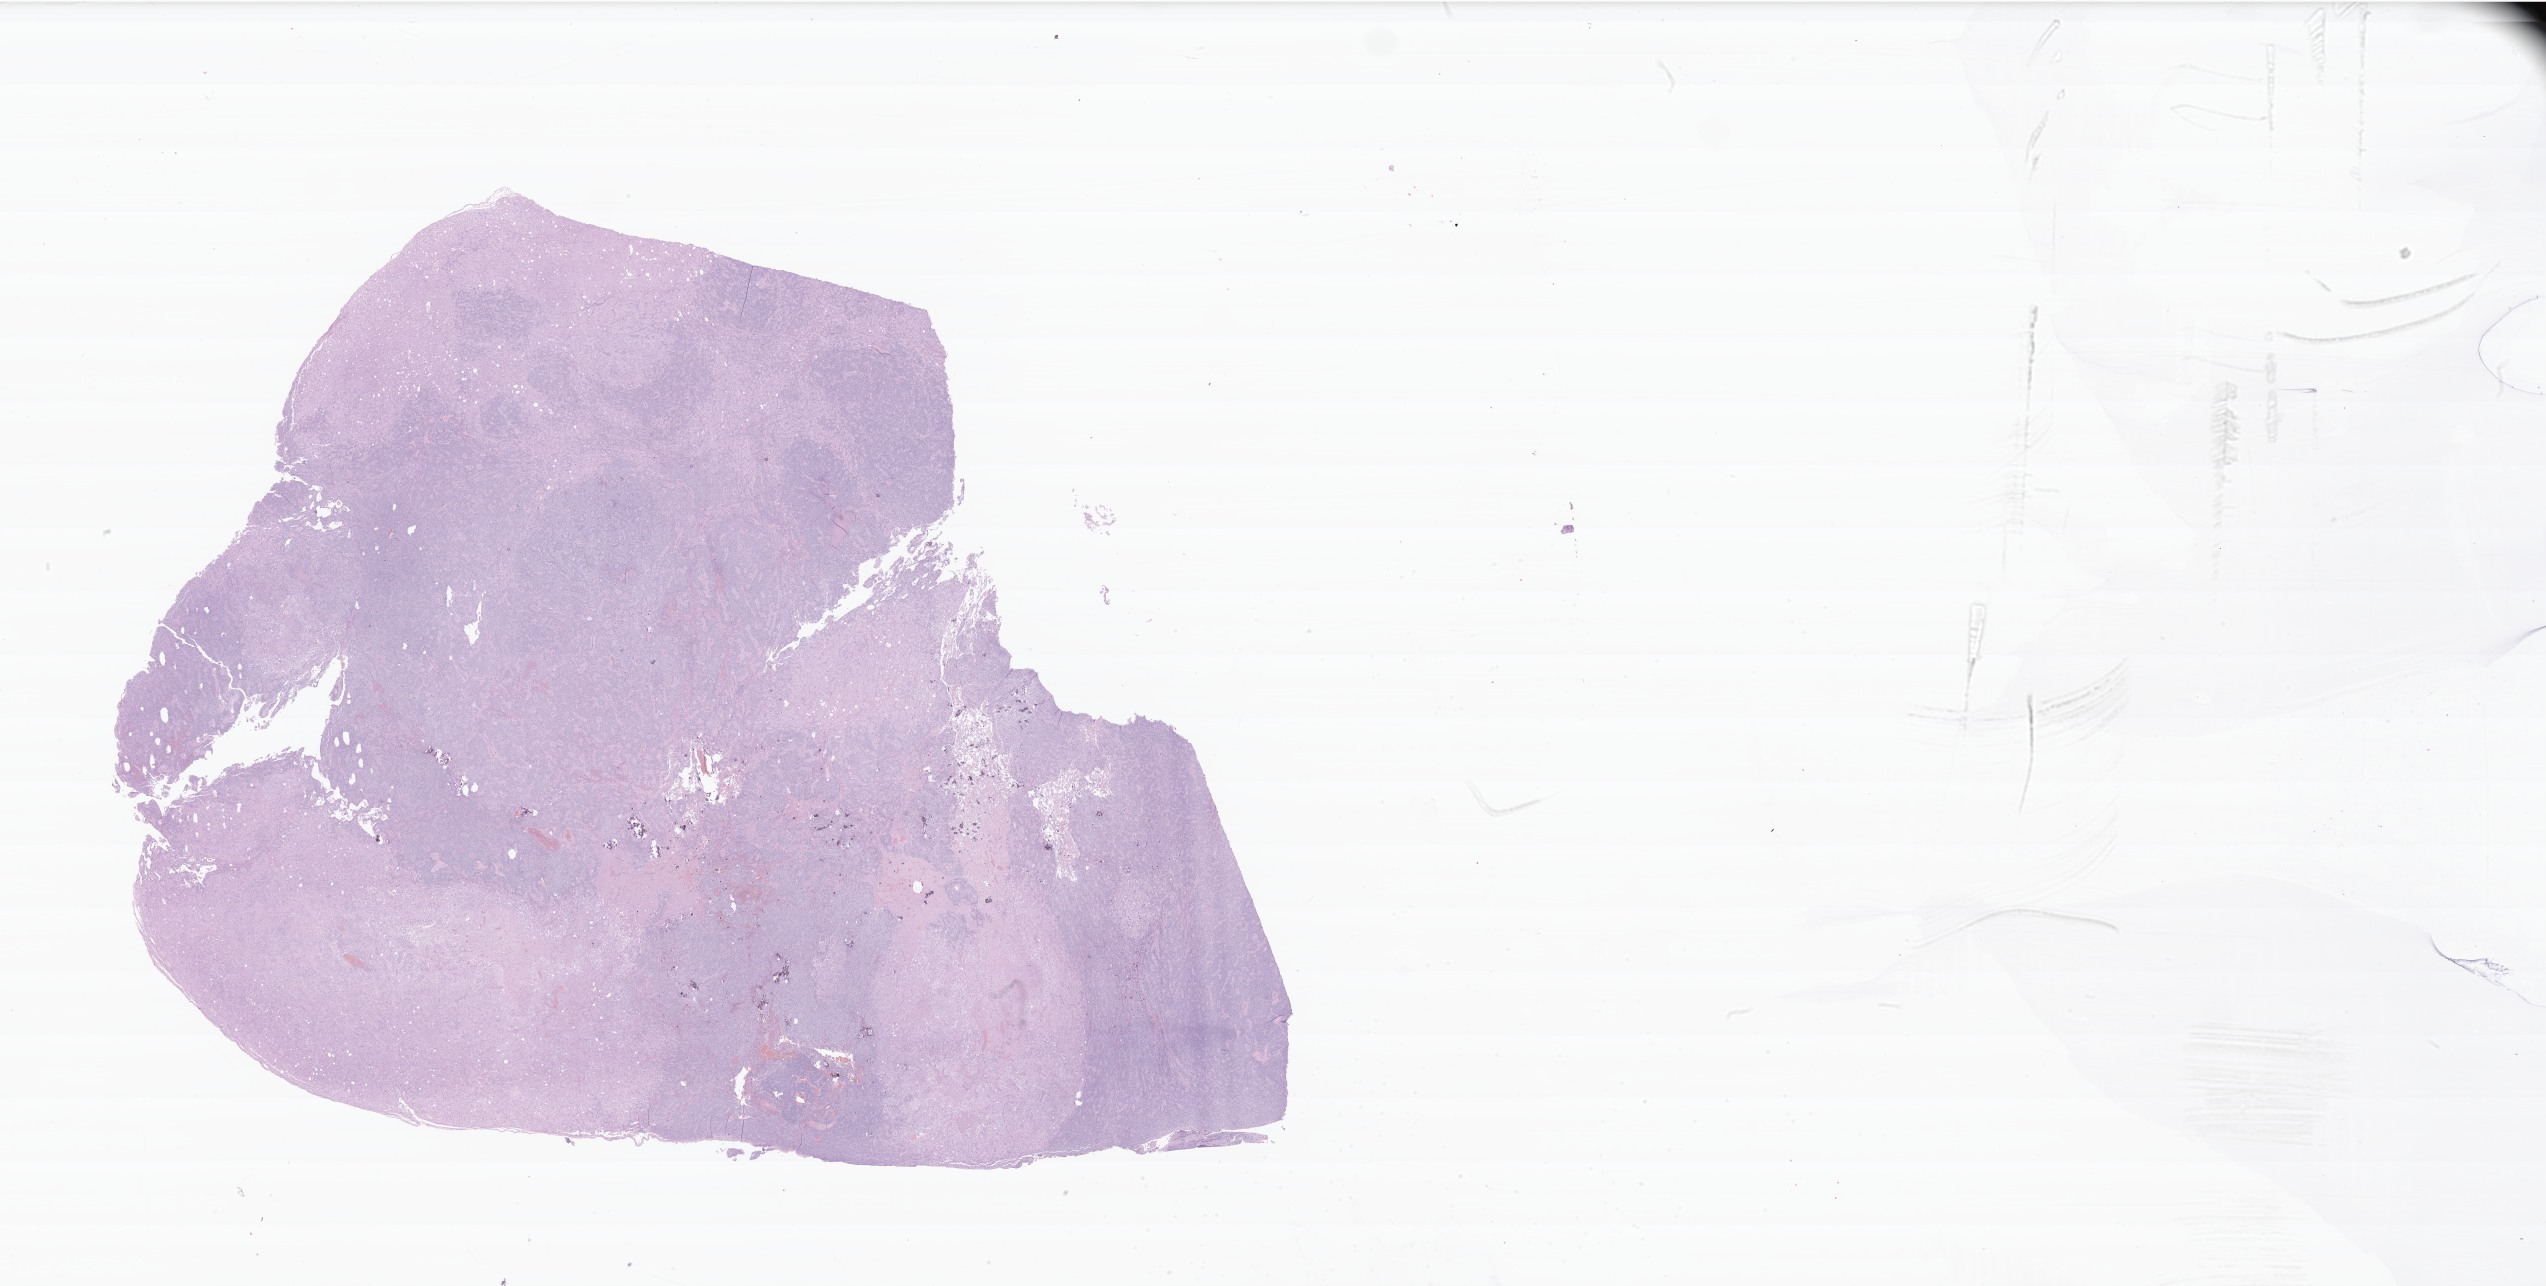
H&E whole-slide image of tumor tissue from the frontal lobe — shown as a low-resolution overview of the whole scanned area (about 42.8 x 21.6 mm), formalin-fixed, paraffin-embedded (FFPE) tissue. Patient male; age 75 months (6 years 3 months).
Diagnosis: Ependymoma, NOS.